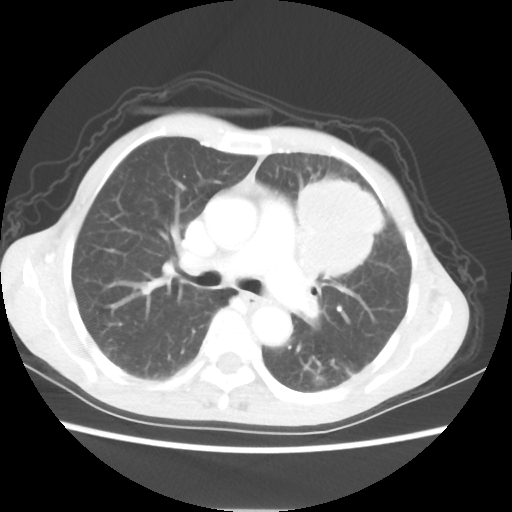
Chest CT, one axial slice. Slice 37 of 56 in the series (ordered by position). Reconstruction kernel STANDARD. Lung window (W 1500 / L -600 HU). 512 × 512 image matrix. Female patient, age 60 years. From the clinical record (not read from this slice): clinical TNM (as recorded): T4 N1 M0.
Annotated regions visible in this slice (rectangle marked by the reading radiologist):
- lung tumour (recorded histology: adenocarcinoma): bounding box [x1, y1, x2, y2] px = [295, 177, 380, 285]